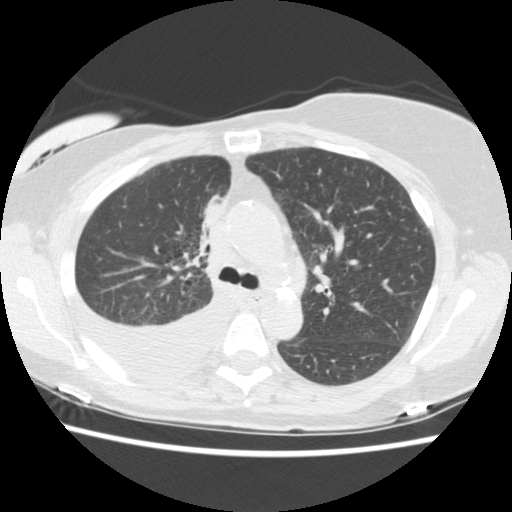
Low-dose screening chest CT, axial slice; third screening round (two years after baseline); lung window (W 1500 / L -600 HU); 2.5 mm slice thickness; 512 × 512 image matrix, field of view 330 × 330 mm. Female participant, aged 56 years at enrolment.
Expert-annotated lung lesion, bounding box <181,189,240,254> (left, top, right, bottom; pixels). The screening reader recorded 2 non-calcified nodules or masses ≥4 mm on this exam (right middle lobe, right lower lobe); which of them this box marks is not recorded. Lung cancer was diagnosed 160 days after this screen: adenocarcinoma, NOS, right upper lobe, stage IIIB (AJCC 6th edition), 8 mm at pathology.